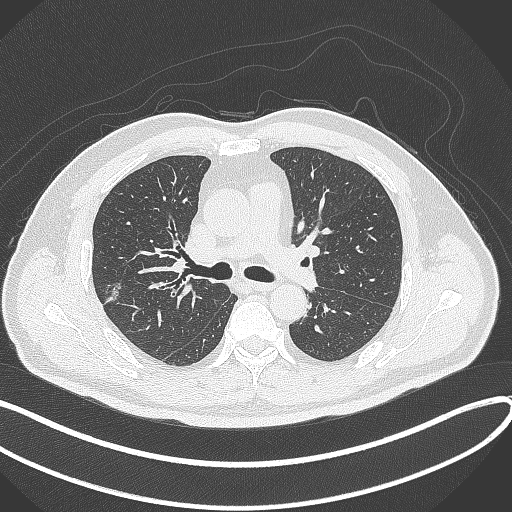
Chest CT, one axial slice. Position 210 of 372 along the scan axis. 120 kVp. Lung window (W 1500 / L -600 HU). 1 mm slice thickness. 512 × 512 image matrix. Male patient, age 60 years. From the clinical record (not read from this slice): clinical TNM (as recorded): T1c N0 M0.
Structures marked on this image (rectangle marked by the reading radiologist):
- lung tumour (recorded histology: adenocarcinoma): bounding box <101,279,126,313> (left, top, right, bottom; pixels)